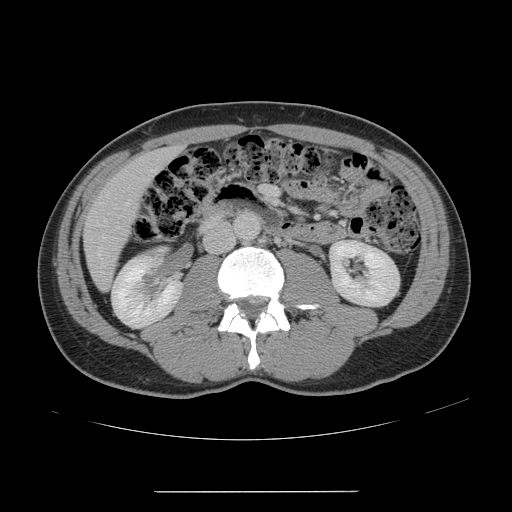
Contrast-enhanced abdominal CT, one axial slice; slice 46 of 178 in the series (ordered by position); intravenous contrast given; soft-tissue window (W 400 / L 40 HU); 512 × 512 image matrix, field of view 401 × 401 mm. Male patient, age 53 years. From the clinical record (not read from this slice): diagnosis: colorectal cancer liver metastases, imaged before liver resection; multiple liver metastases: yes.
Structures marked on this image (expert manual segmentation):
- hepatic veins: bounding box (x1, y1, x2, y2) in pixels: (97, 169, 158, 259)
- liver: (85, 148, 177, 290)